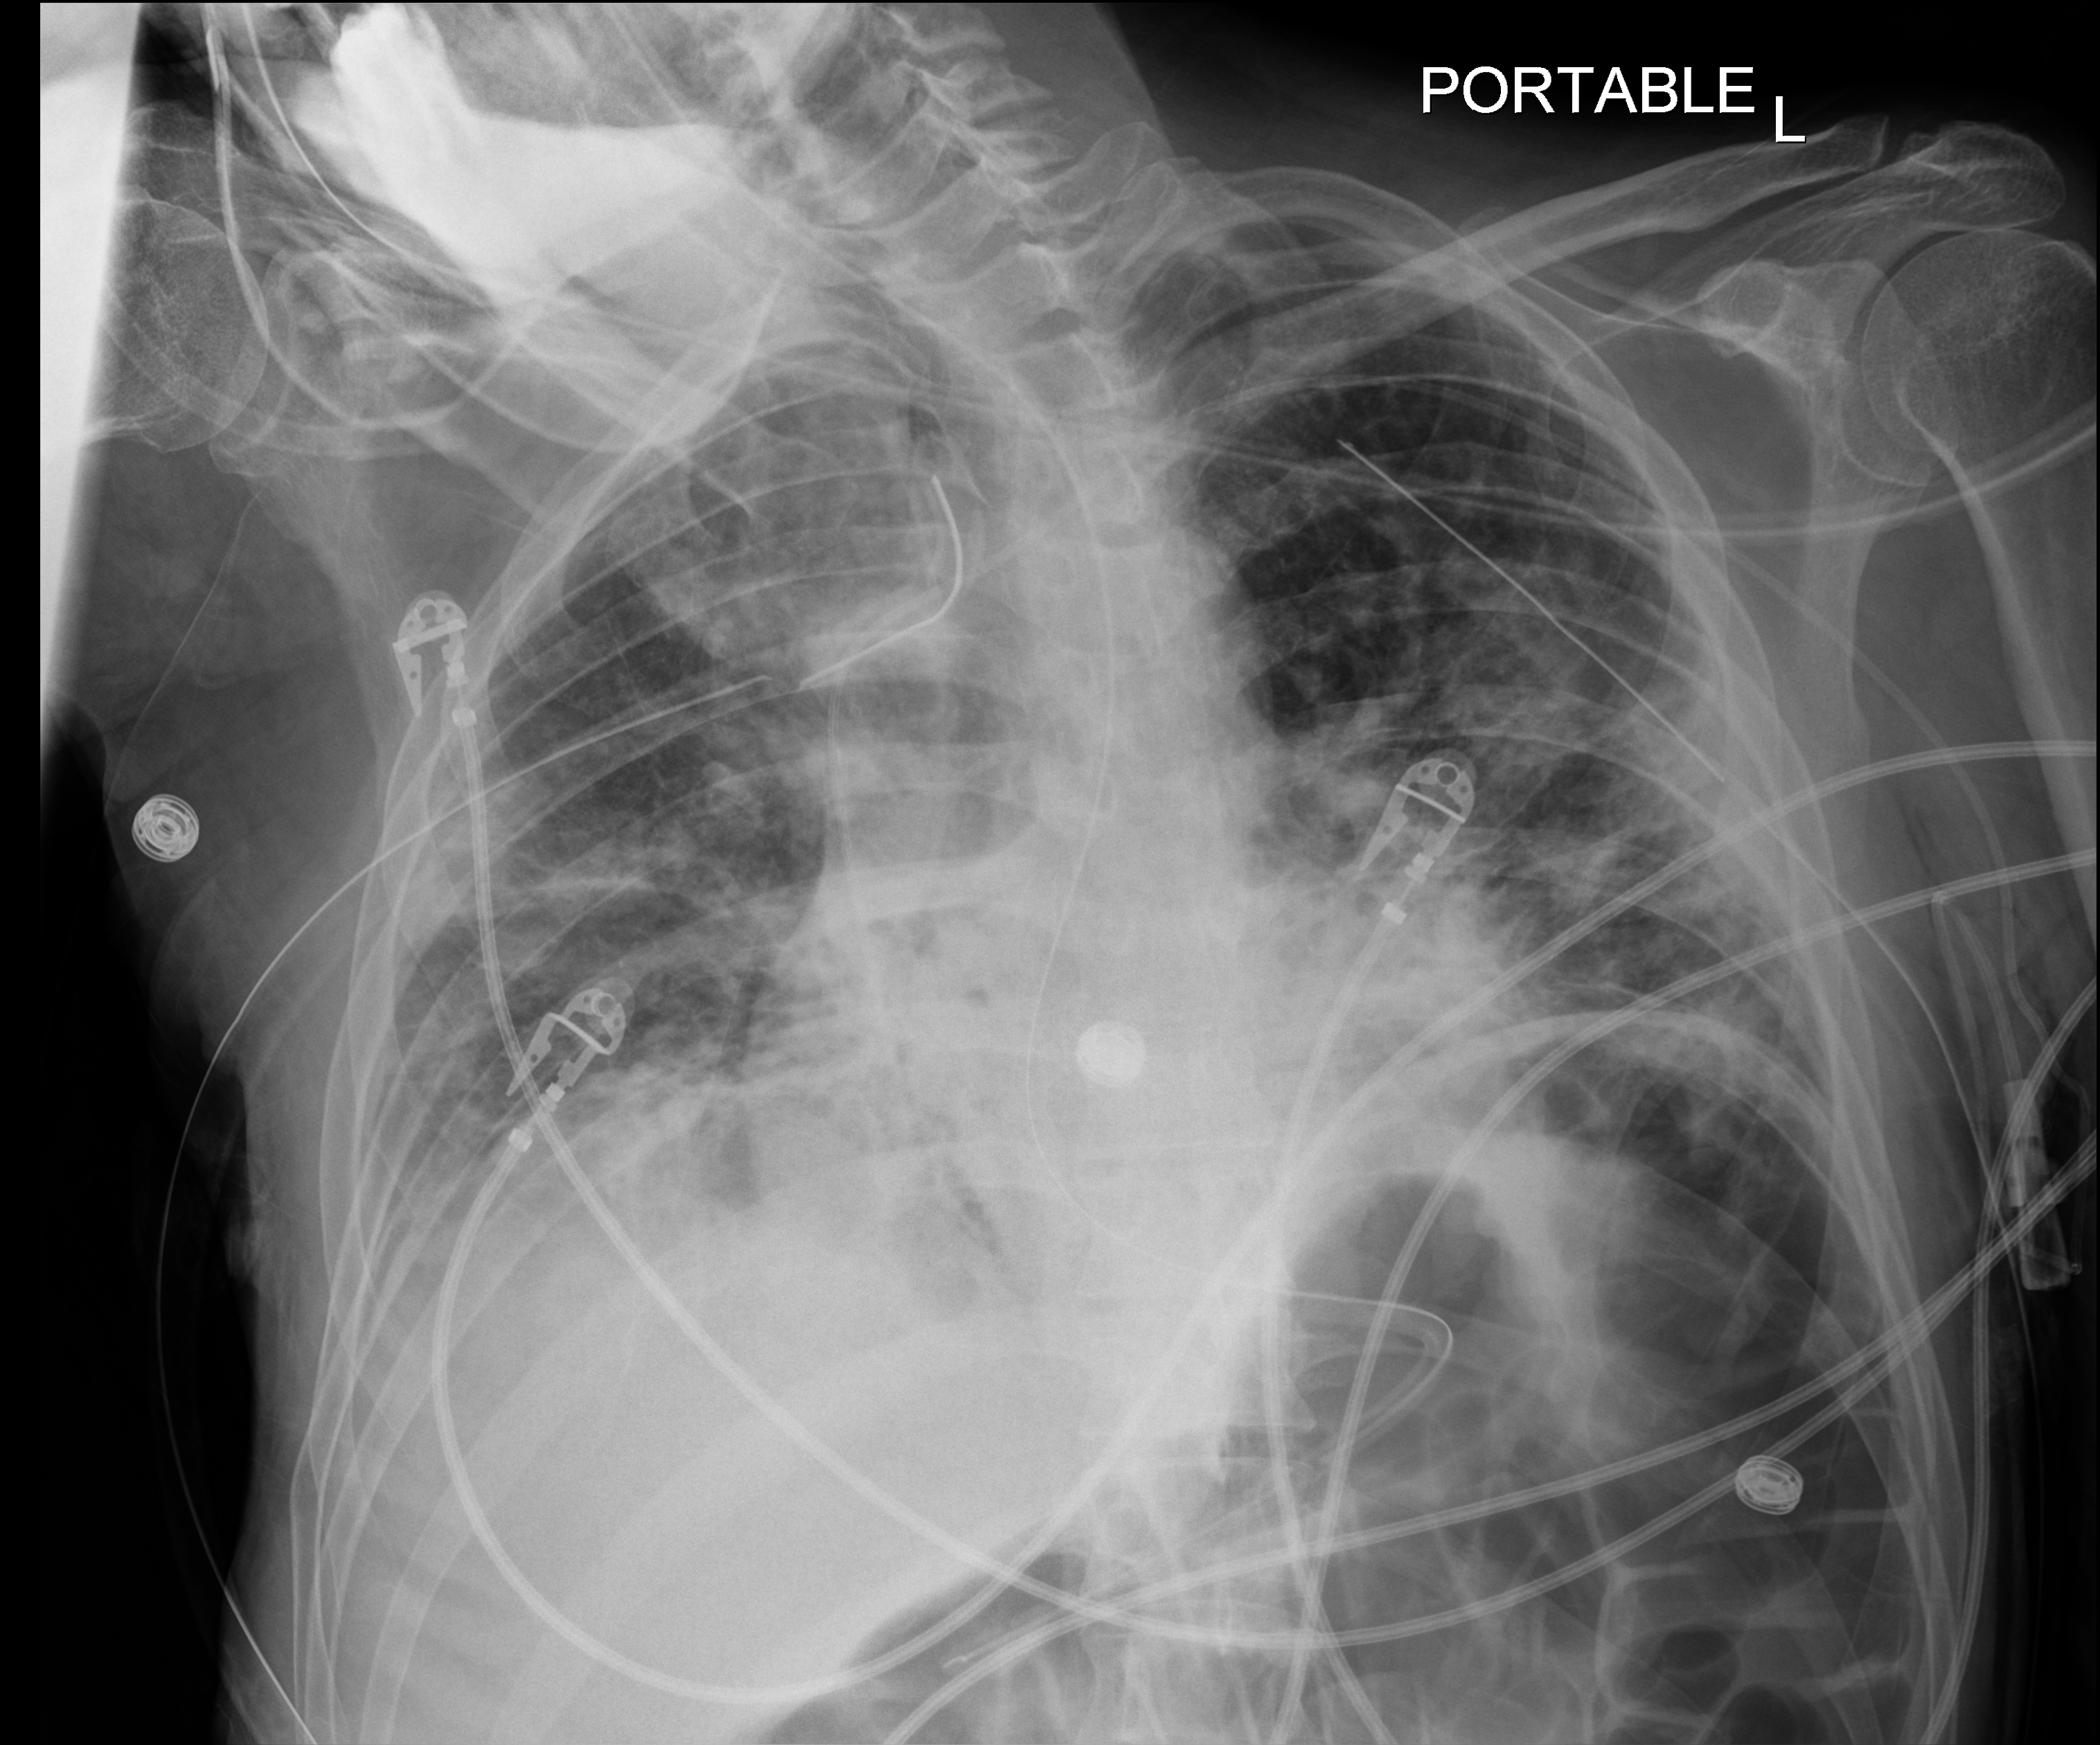
Chest radiograph (digital radiography). Male patient hospitalised with COVID-19, age 18–59 years.
Admission-level facts for this patient (not findings on this image; timing relative to this image not recorded): smoking status (admission record): never; admitted to intensive care during this hospital stay: yes; mechanically ventilated during this hospital stay: yes.